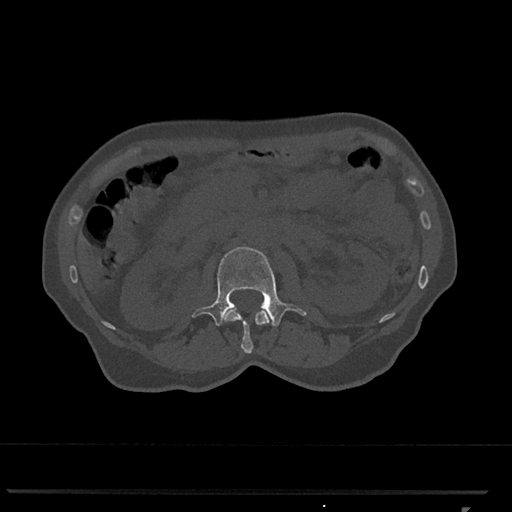
CT including the spine, one axial slice; slice 359 of 793 in the series (ordered by position); 120 kVp; bone window (W 1800 / L 400 HU); 0.5 mm slice thickness; 512 × 512 image matrix. Patient: female, 62 years. From the clinical record (not read from this slice): primary cancer: renal.
Structures marked on this image (semi-automatic segmentation, software-assisted and operator-edited):
- L1 vertebra: bounding box (x1, y1, x2, y2) in pixels: (224, 308, 272, 354)
- L2 vertebra: (192, 247, 307, 327)